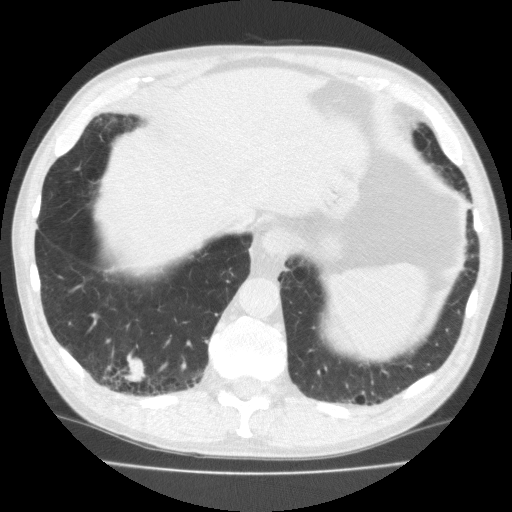
Axial slice from a low-dose chest CT screening exam. Second screening round (one year after baseline). Lung window (W 1500 / L -600 HU). 2 mm slice thickness. Standard (soft-tissue) reconstruction kernel (FC10). Slice 146 of 195 in the series. Male, age 70 years at enrolment. Current smoker at enrolment.
Expert-annotated lung lesion, bounding box <93,346,160,398> (left, top, right, bottom; pixels). The exam's reader record, not a measurement of the box and not confirmed to be the same lesion: non-calcified nodule or mass ≥4 mm, right lower lobe, 18 × 13 mm, spiculated (stellate) margins, soft tissue attenuation, pre-existing on the prior screen: no. Lung cancer was diagnosed 64 days after this screen: squamous cell carcinoma, NOS, right lower lobe, moderately differentiated (G2), stage IA (AJCC 6th edition), 20 mm at pathology.